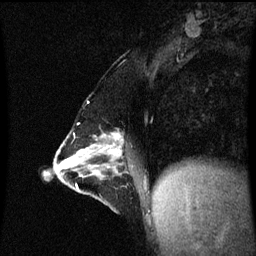
Breast MRI (dynamic contrast-enhanced), one sagittal slice; slice 26 of 60 in the series (ordered by position); dynamic contrast-enhanced series, image 2 of 3 at this slice position (ordered by acquisition); 1.5 T; TE 4.2 ms, TR 8.9 ms; 256 × 256 image matrix, field of view 200 × 200 mm. Female patient, age 47 years. From the clinical record (not read from this slice): setting: breast cancer imaged before/during neoadjuvant chemotherapy; receptor status: HR-positive, HER2-negative.
Annotated regions visible in this slice (semi-automatic segmentation, software-assisted and operator-edited):
- analysis volume of interest (the breast-tissue region the enhancement analysis was run in; not a lesion): bounding box <53,132,138,209> (left, top, right, bottom; pixels)
- tumour enhancement mask (voxels above the 70 % enhancement threshold inside the analysis volume of interest): <78,134,123,173>